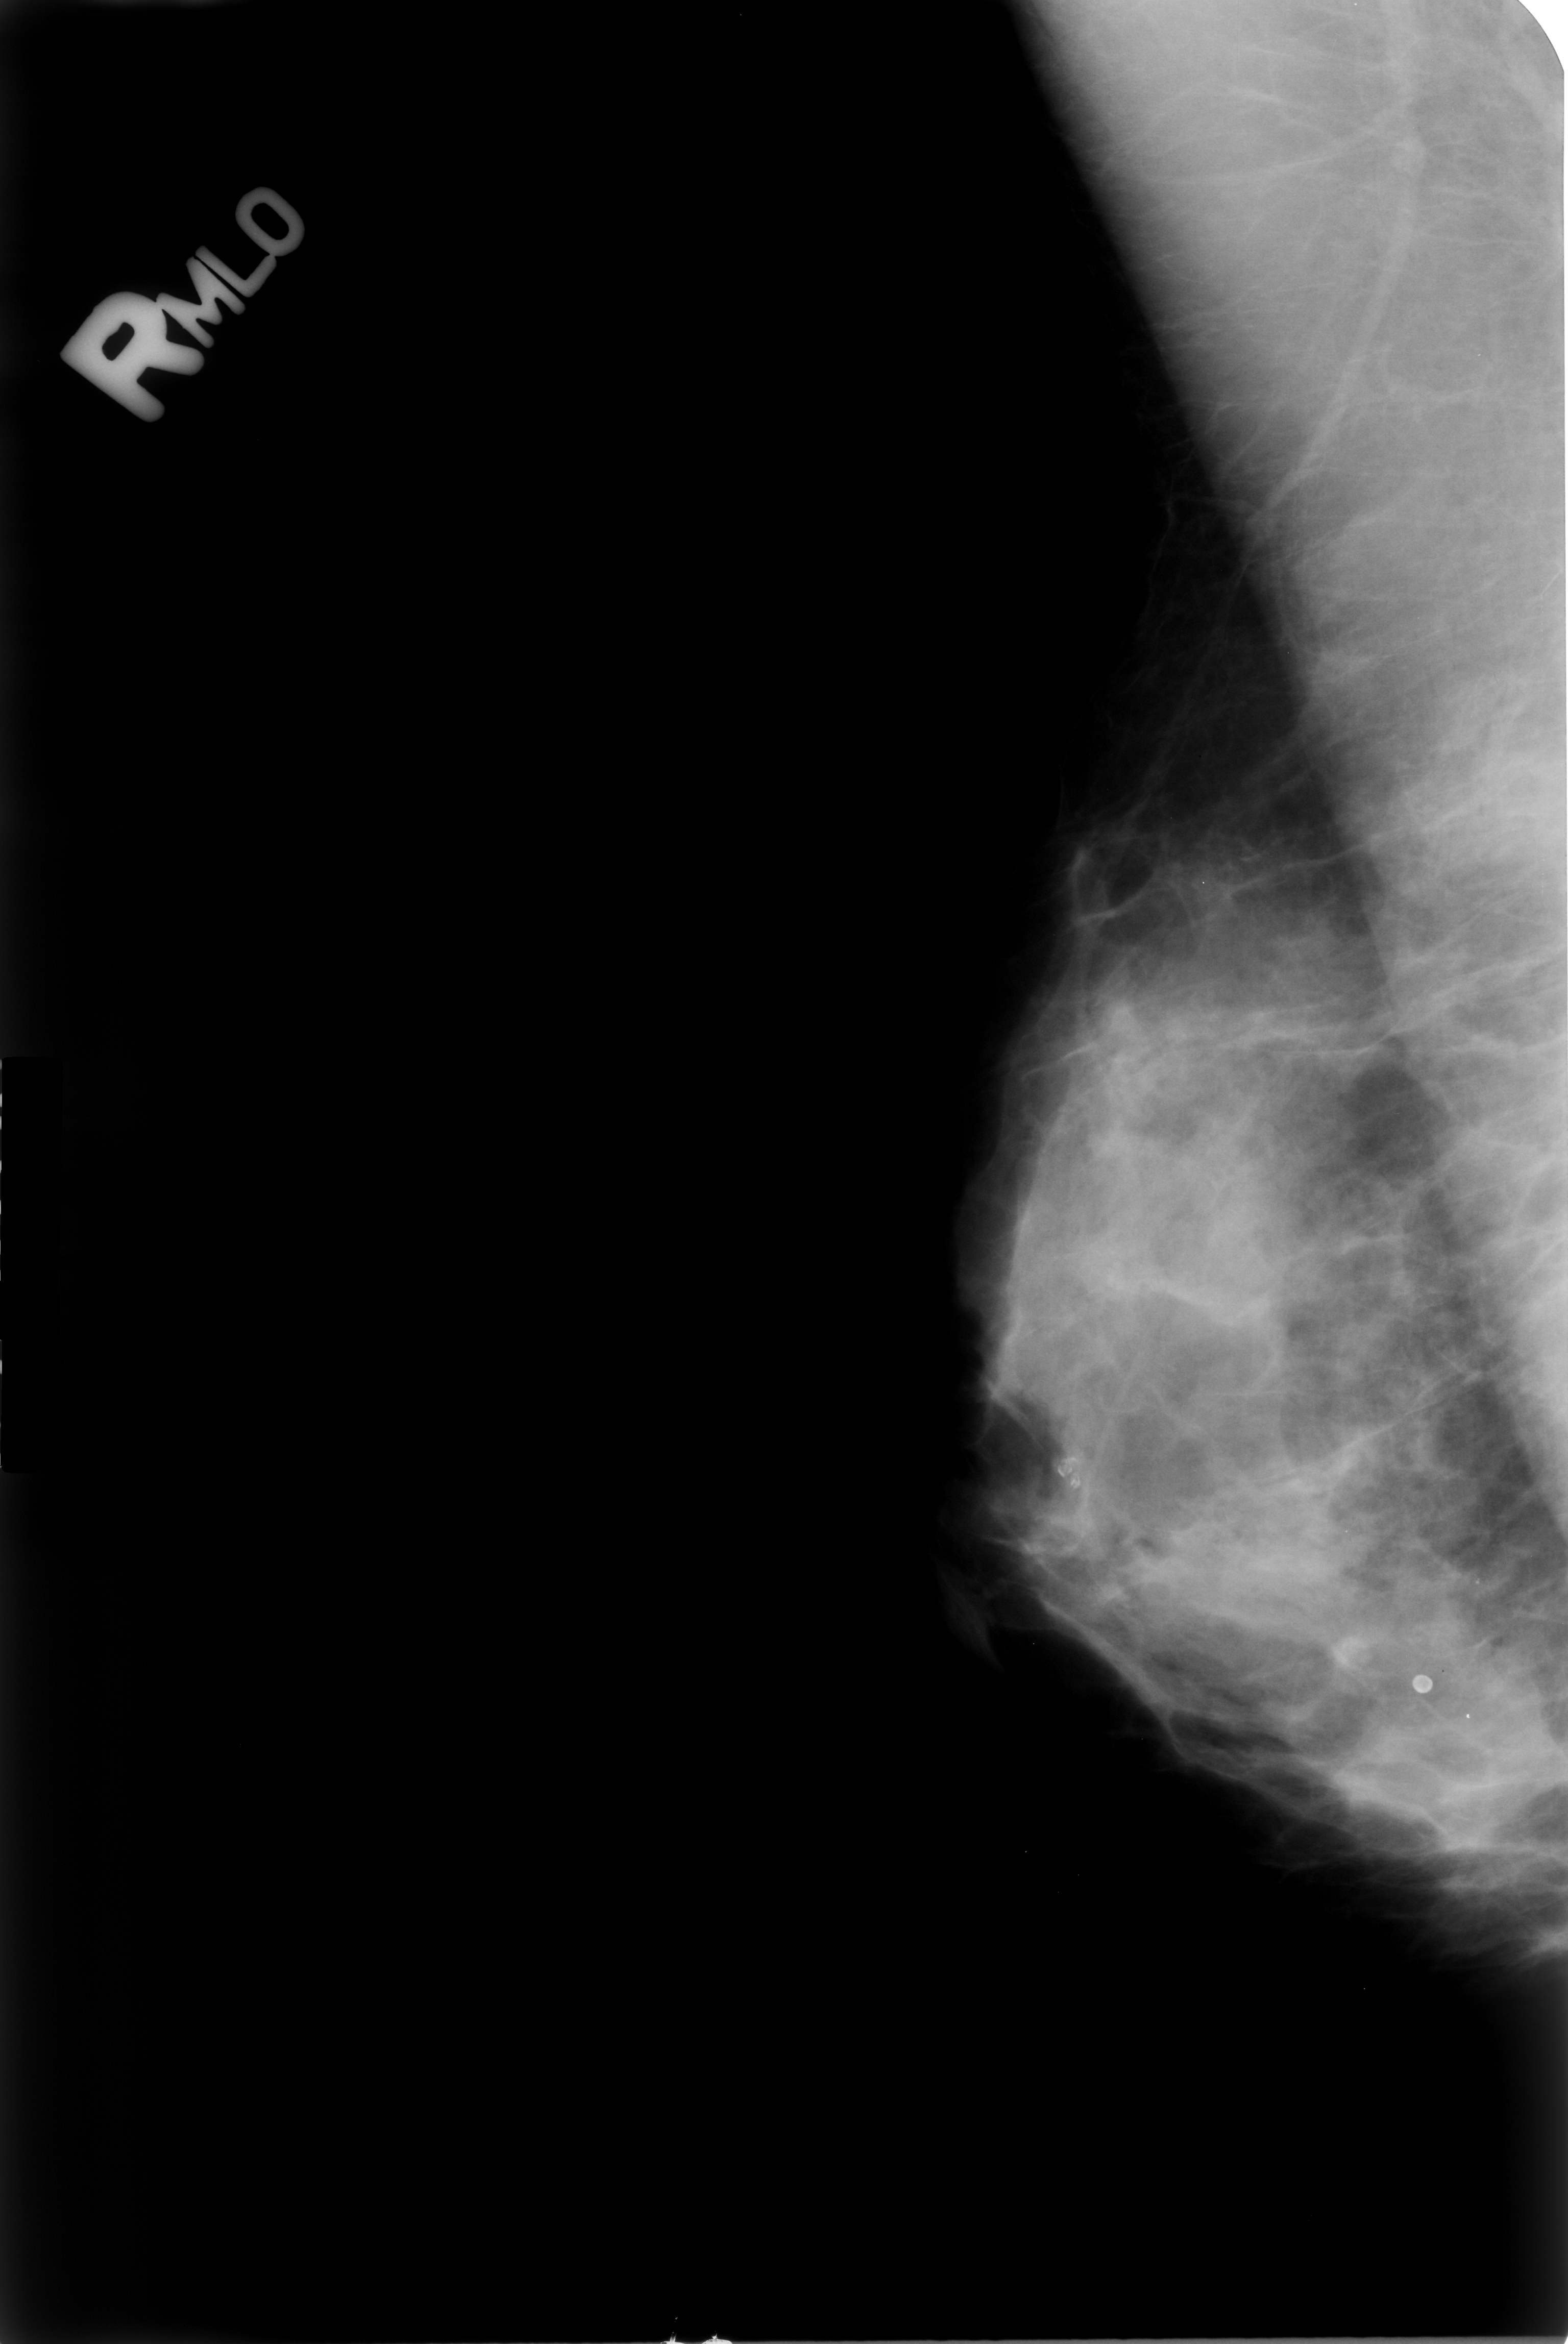
Mammogram (digitized film); right breast; MLO view; BI-RADS breast density category 3 (scale 1–4); 1568 × 2344 image matrix.
Expert-marked regions of interest on this image (one box per marked abnormality):
- Finding 1 of 2: calcifications, morphology lucent center; BI-RADS assessment category 2; subtlety rating 5 on a 1 (subtle) to 5 (obvious) scale; outcome (as recorded, no biopsy): benign without callback (not worked up further): box from (x=1020, y=1392) to (x=1120, y=1504) px
- Finding 2 of 2: calcifications, morphology lucent center; BI-RADS assessment category 2; subtlety rating 5 on a 1 (subtle) to 5 (obvious) scale; outcome (as recorded, no biopsy): benign without callback (not worked up further): (x=1392, y=1641)–(x=1467, y=1737)